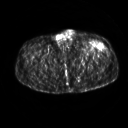
FDG PET of an extremity soft-tissue mass (from a PET/CT study), one axial slice. Slice 257 of 267 in the series (ordered by position). 3.27 mm slice thickness. 128 × 128 image matrix. Patient: male, 64 years. From the clinical record (not read from this slice): histological type: extraskeletal osteosarcoma; grade: high; site of the primary tumour: thigh.
Structures marked on this image (expert contour drawn on MRI and transferred to this co-registered scan by the dataset authors):
- gross tumour volume (mass): bounding box [x1, y1, x2, y2] px = [92, 42, 105, 49]